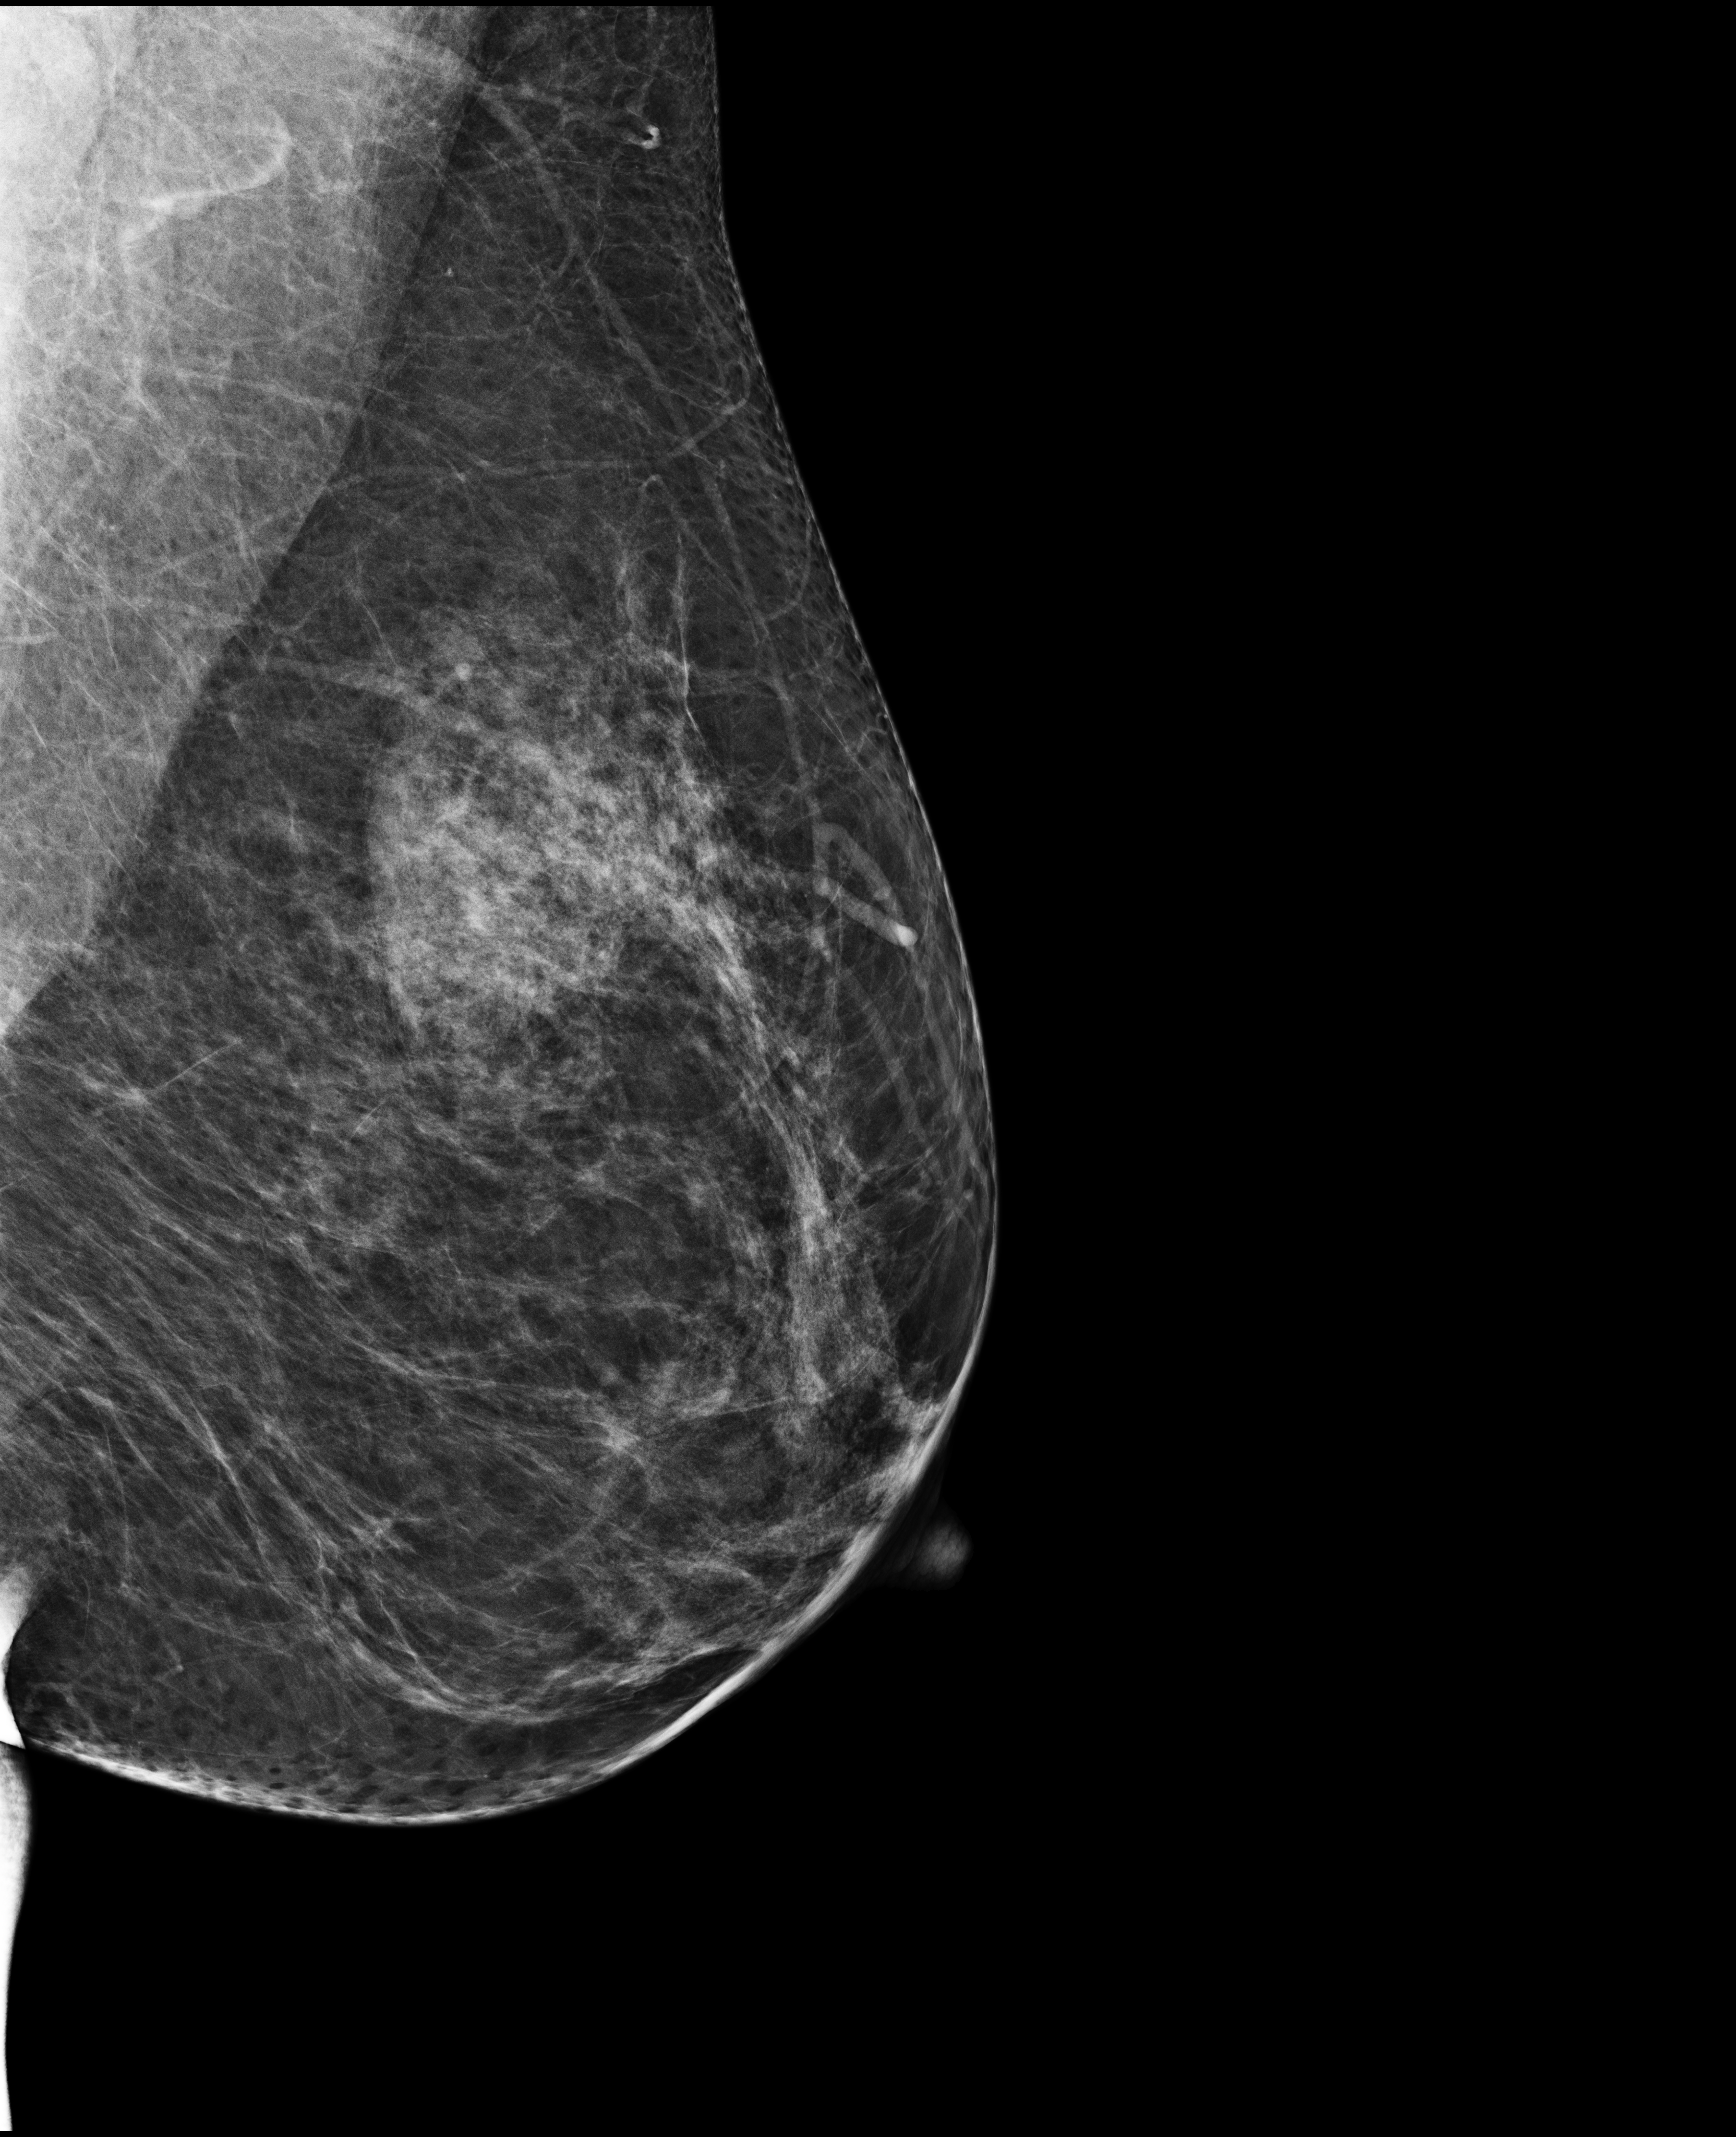
Annual screening mammography examination, compressed breast thickness 79 mm. Female patient, age 47 years.
Image type: full-field digital mammogram. Breast: left. Projection: mediolateral oblique (MLO) view.